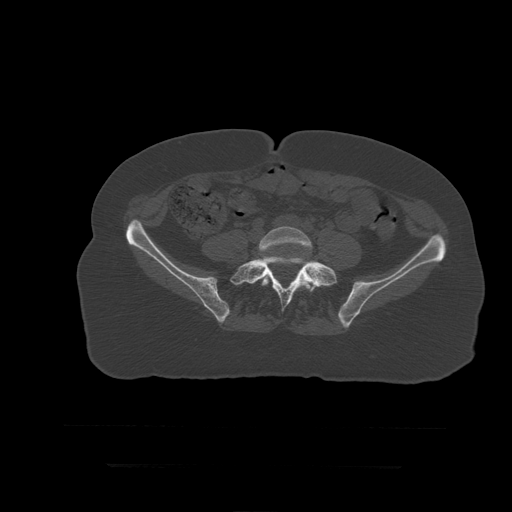
CT including the spine, one axial slice. Reconstruction kernel STANDARD. 120 kVp. Bone window (W 1800 / L 400 HU). 1.25 mm slice thickness. 512 × 512 image matrix, field of view 450 × 450 mm. Patient age 41 years. From the clinical record (not read from this slice): primary cancer: breast.
Structures marked on this image (semi-automatically segmented with operator editing):
- L5 vertebra: bounding box [x1, y1, x2, y2] px = [259, 227, 317, 292]